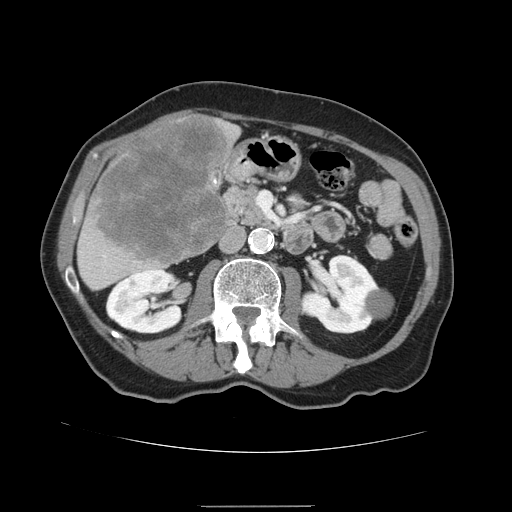
Contrast-enhanced abdominal CT, one axial slice. Slice 57 of 168 in the series (ordered by position). 120 kVp. Intravenous contrast given. Soft-tissue window (W 400 / L 40 HU). 512 × 512 image matrix, field of view 386 × 386 mm. Male patient, age 74 years. Case-level facts recorded for this patient, not image findings: diagnosis: colorectal cancer liver metastases, imaged before liver resection; multiple liver metastases: no.
Outlined on this slice (manually delineated by an expert):
- liver: bounding box (x1, y1, x2, y2) in pixels: (77, 114, 242, 291)
- liver metastasis: (94, 118, 232, 266)